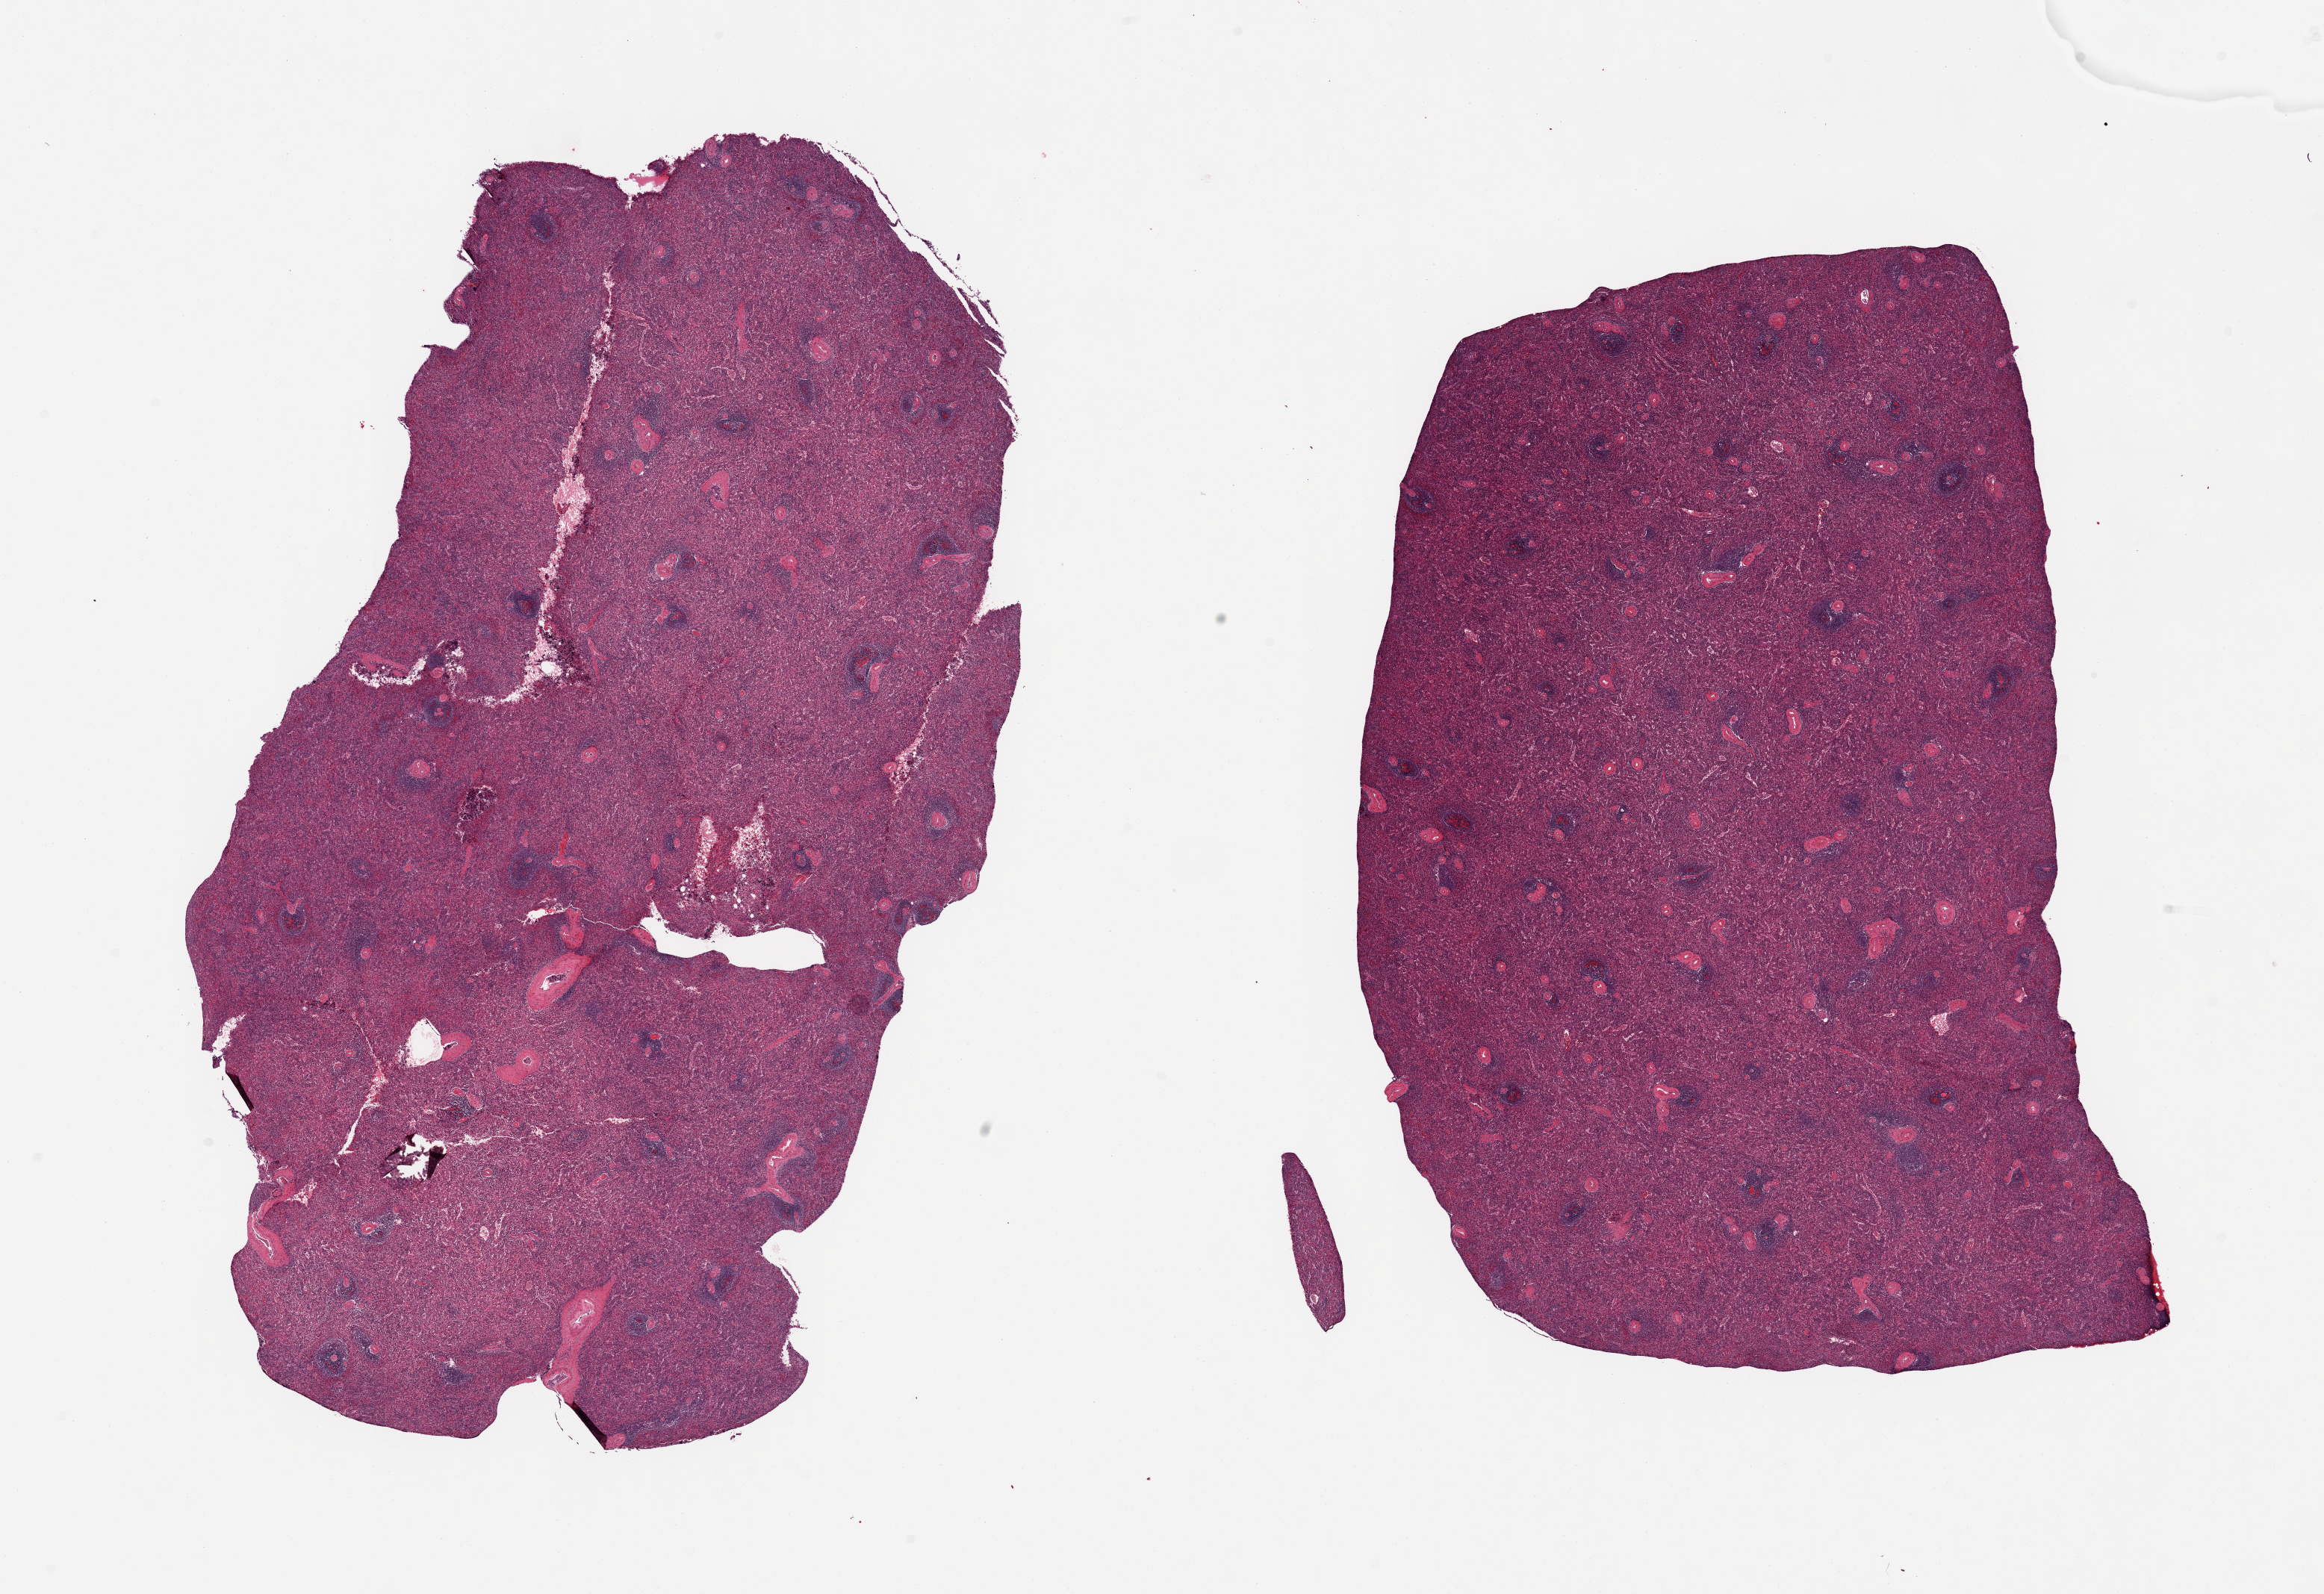
Haematoxylin and eosin whole-slide image — shown as a low-resolution overview of the whole scanned area (about 24.6 x 16.9 mm, slide scanned at 20x). PAXgene-fixed, paraffin-embedded tissue. Section of spleen (target tissue). Donor tissue sample. Donor sex: female.
• pathologist's review note for this sample: 2 pieces, no abnormalities